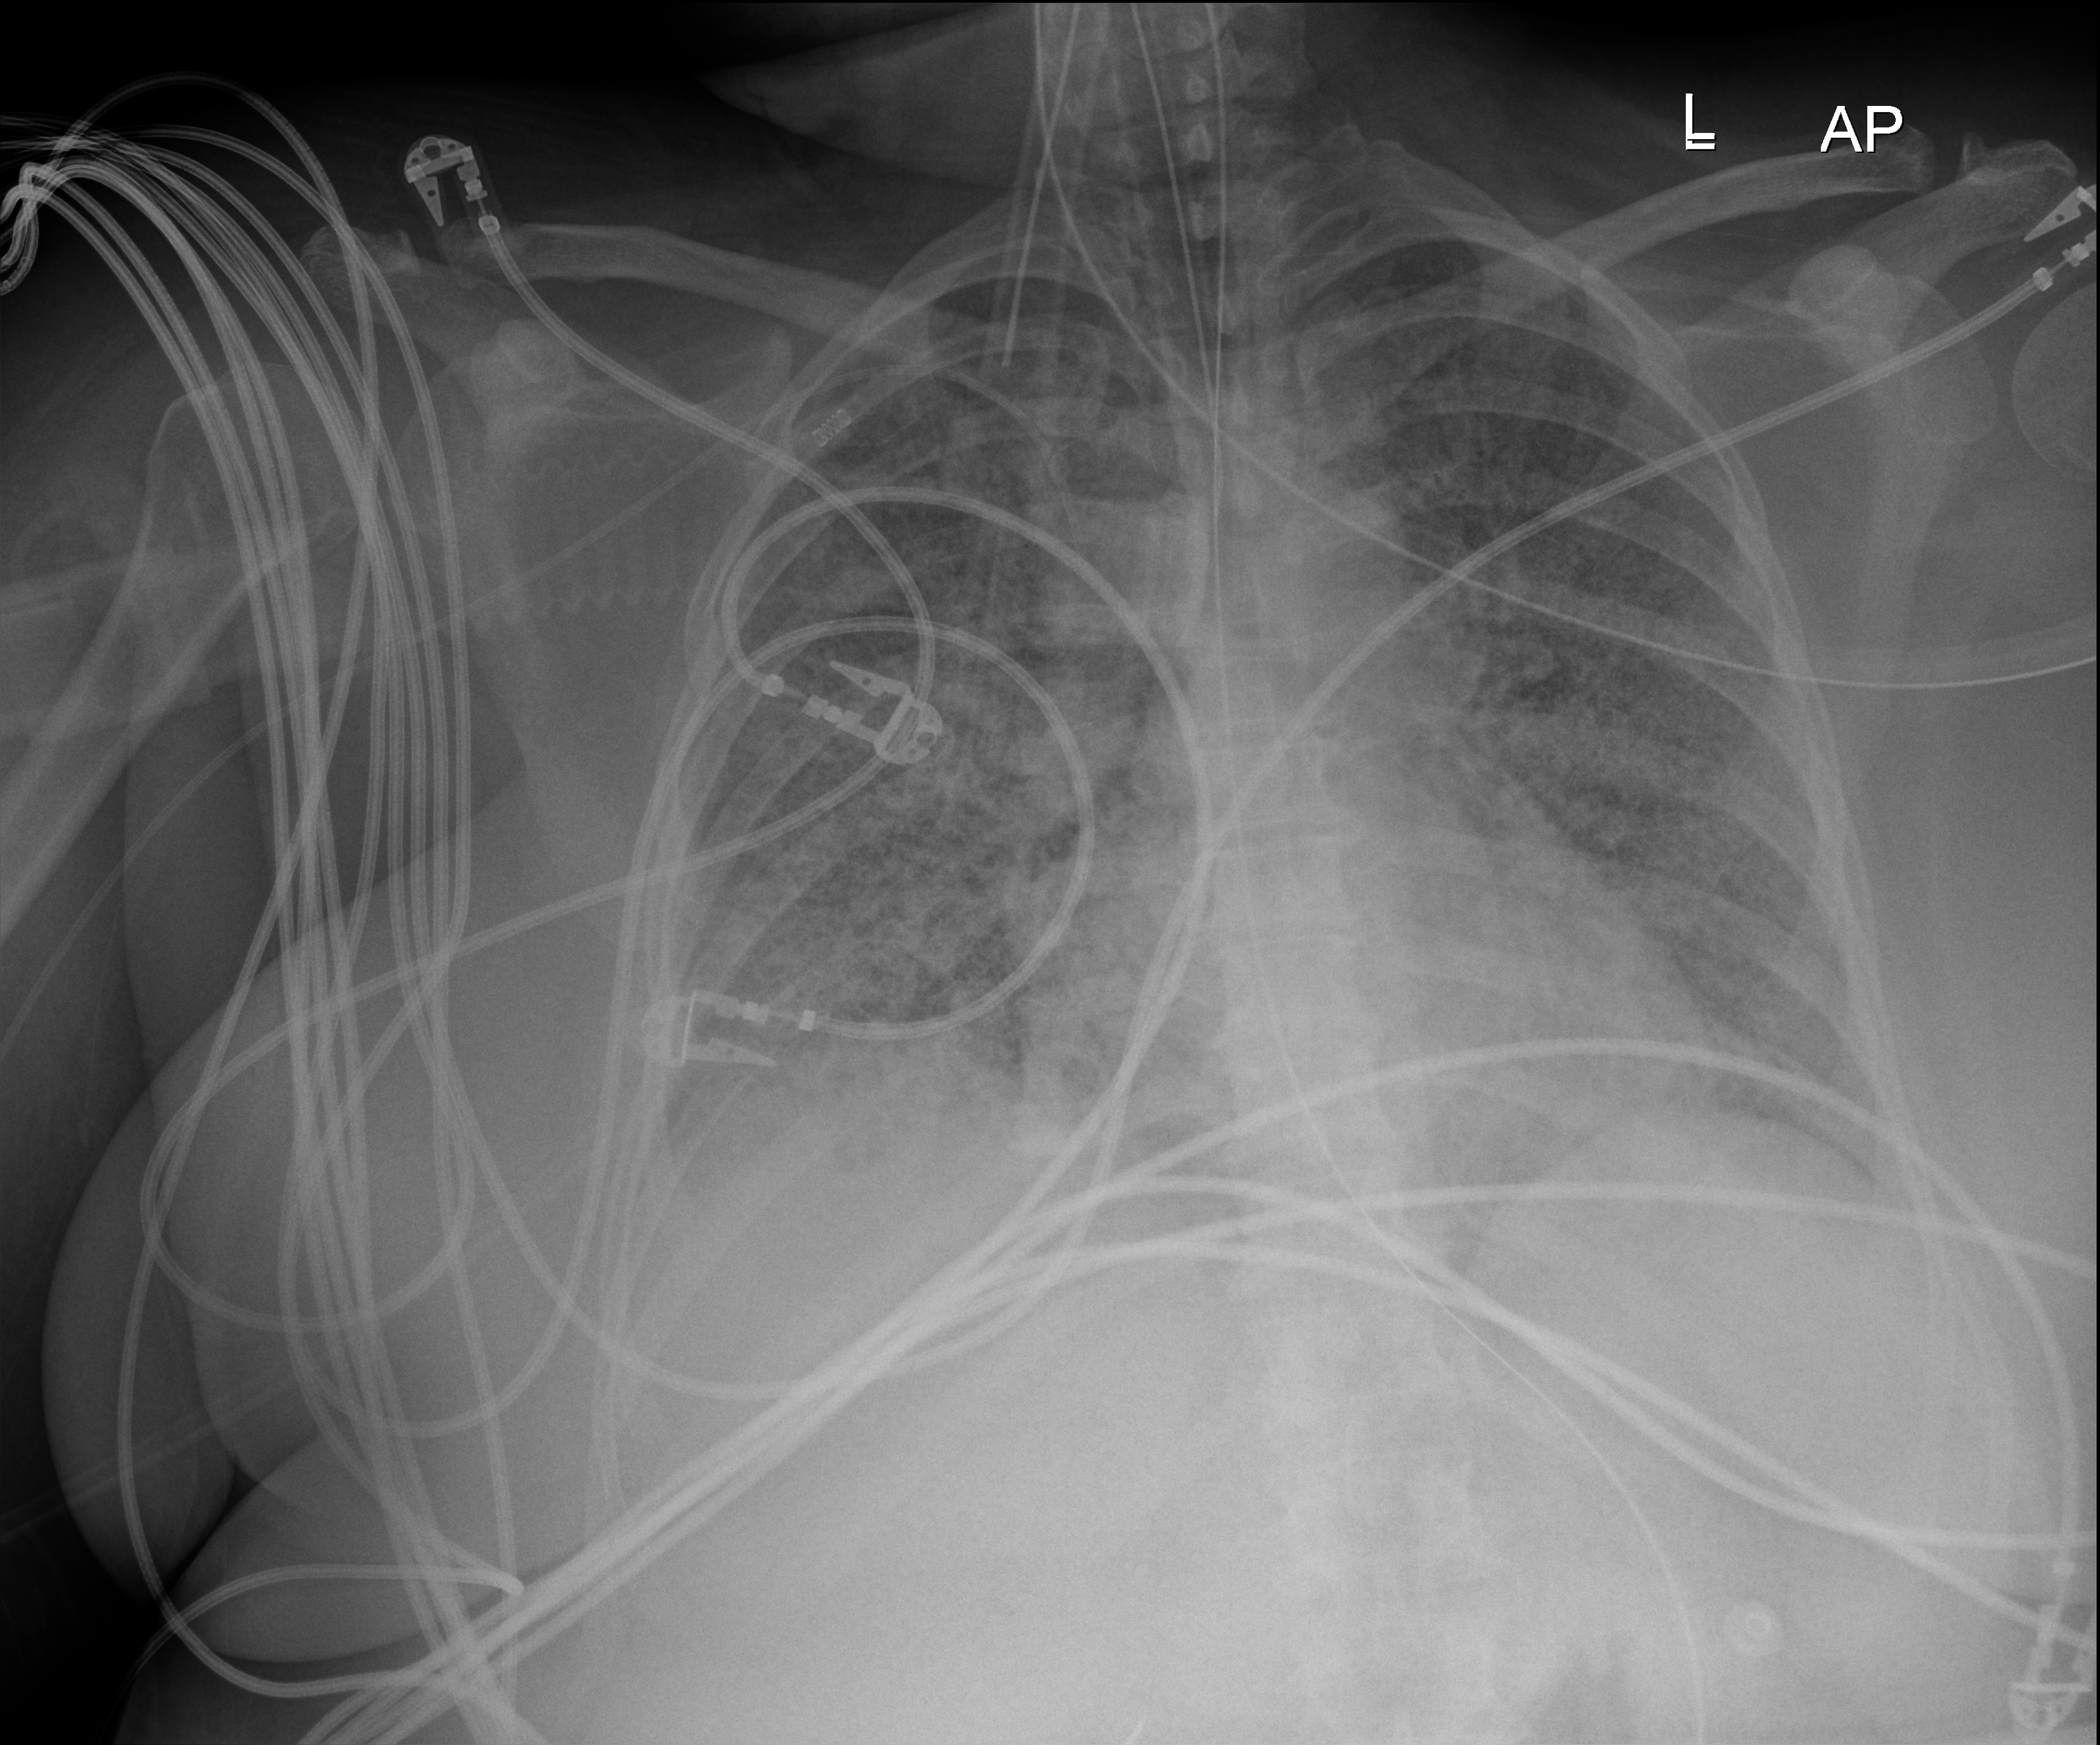
Bedside chest radiograph (digital radiography). Female patient hospitalised with COVID-19, age 18–59 years.
Admission-level facts for this patient (not findings on this image; timing relative to this image not recorded): admitted to intensive care during this hospital stay: yes; mechanically ventilated during this hospital stay: yes.